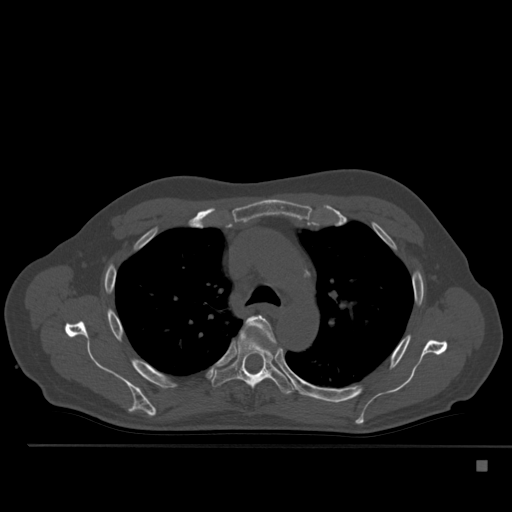
CT including the spine, one axial slice; slice 370 of 517 in the series (ordered by position); 120 kVp; bone window (W 1800 / L 400 HU); 512 × 512 image matrix, field of view 408 × 408 mm. Patient: male, 70 years. Case-level facts recorded for this patient, not image findings: primary cancer: renal.
Annotated regions visible in this slice (semi-automatic segmentation, software-assisted and operator-edited):
- T4 vertebra: bounding box (x1, y1, x2, y2) in pixels: (247, 315, 275, 343)
- T5 vertebra: (211, 330, 295, 394)